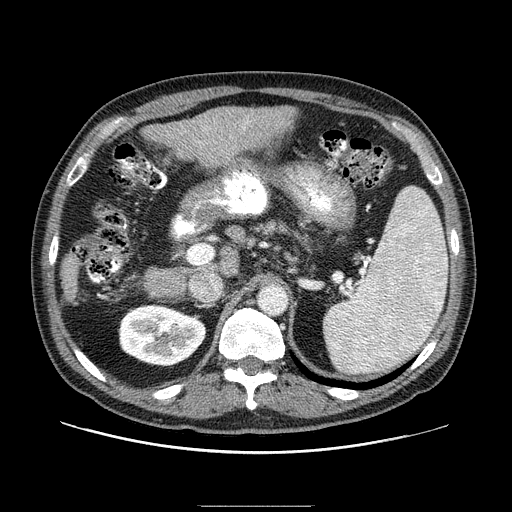
Contrast-enhanced abdominal CT (liver protocol), one axial slice; slice 46 of 99 in the series (ordered by position); 100 kVp; one of 2 acquisitions stored at this slice position; soft-tissue window (W 400 / L 40 HU); 512 × 512 image matrix. From the clinical record (not read from this slice): diagnosis: hepatocellular carcinoma (patient treated with transarterial chemoembolisation; whether this scan precedes or follows treatment is not stated here); TNM stage (as recorded): Stage-II; Child-Pugh class: A; tumour differentiation: well differentiated; tumour nodularity: multinodular.
Outlined on this slice (semi-automatically segmented with operator editing):
- liver parenchyma outside the tumour (the mass and vessels are separate outlines, so this box may not span the whole liver): bounding box (x1, y1, x2, y2) in pixels: (60, 106, 296, 302)